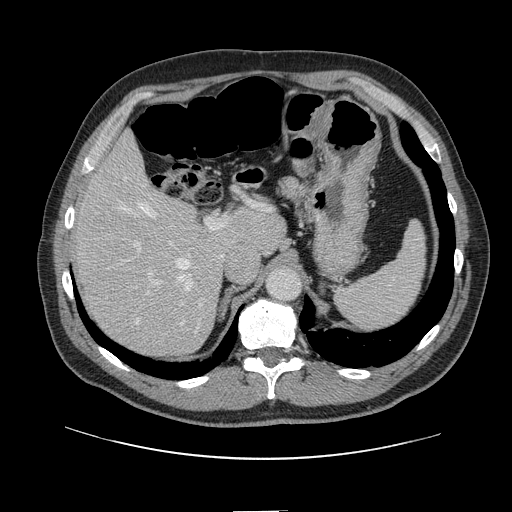
Contrast-enhanced abdominal CT, one axial slice. Slice 94 of 161 in the series (ordered by position). Intravenous contrast given. Soft-tissue window (W 400 / L 40 HU). 512 × 512 image matrix. Male patient, age 66 years. From the clinical record (not read from this slice): diagnosis: colorectal cancer liver metastases, imaged before liver resection; multiple liver metastases: no; largest metastasis: 3.5 cm.
Structures marked on this image (expert manual segmentation):
- hepatic veins: bounding box (x1, y1, x2, y2) in pixels: (118, 177, 191, 323)
- liver: (78, 137, 284, 355)
- planned liver remnant (the part of the liver to remain after resection): (78, 137, 284, 304)
- portal vein (with intrahepatic branches): (118, 217, 225, 314)